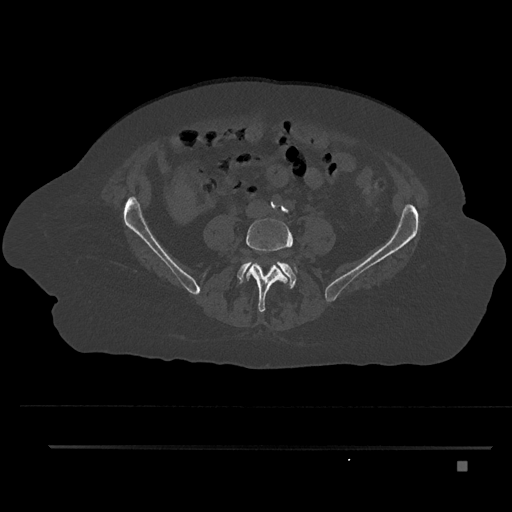
CT including the spine, one axial slice; position 69 of 797 along the scan axis; reconstruction kernel Br40s/3; 120 kVp; bone window (W 1800 / L 400 HU); 0.5 mm slice thickness; 512 × 512 image matrix, field of view 437 × 437 mm. Patient: female, 76 years. Case-level facts recorded for this patient, not image findings: primary cancer: lung; vertebrae with lytic lesions (as recorded): T11, L3.
Outlined on this slice (semi-automatically segmented with operator editing):
- L4 vertebra: bounding box (x1, y1, x2, y2) in pixels: (246, 218, 297, 313)
- L5 vertebra: (237, 261, 297, 288)